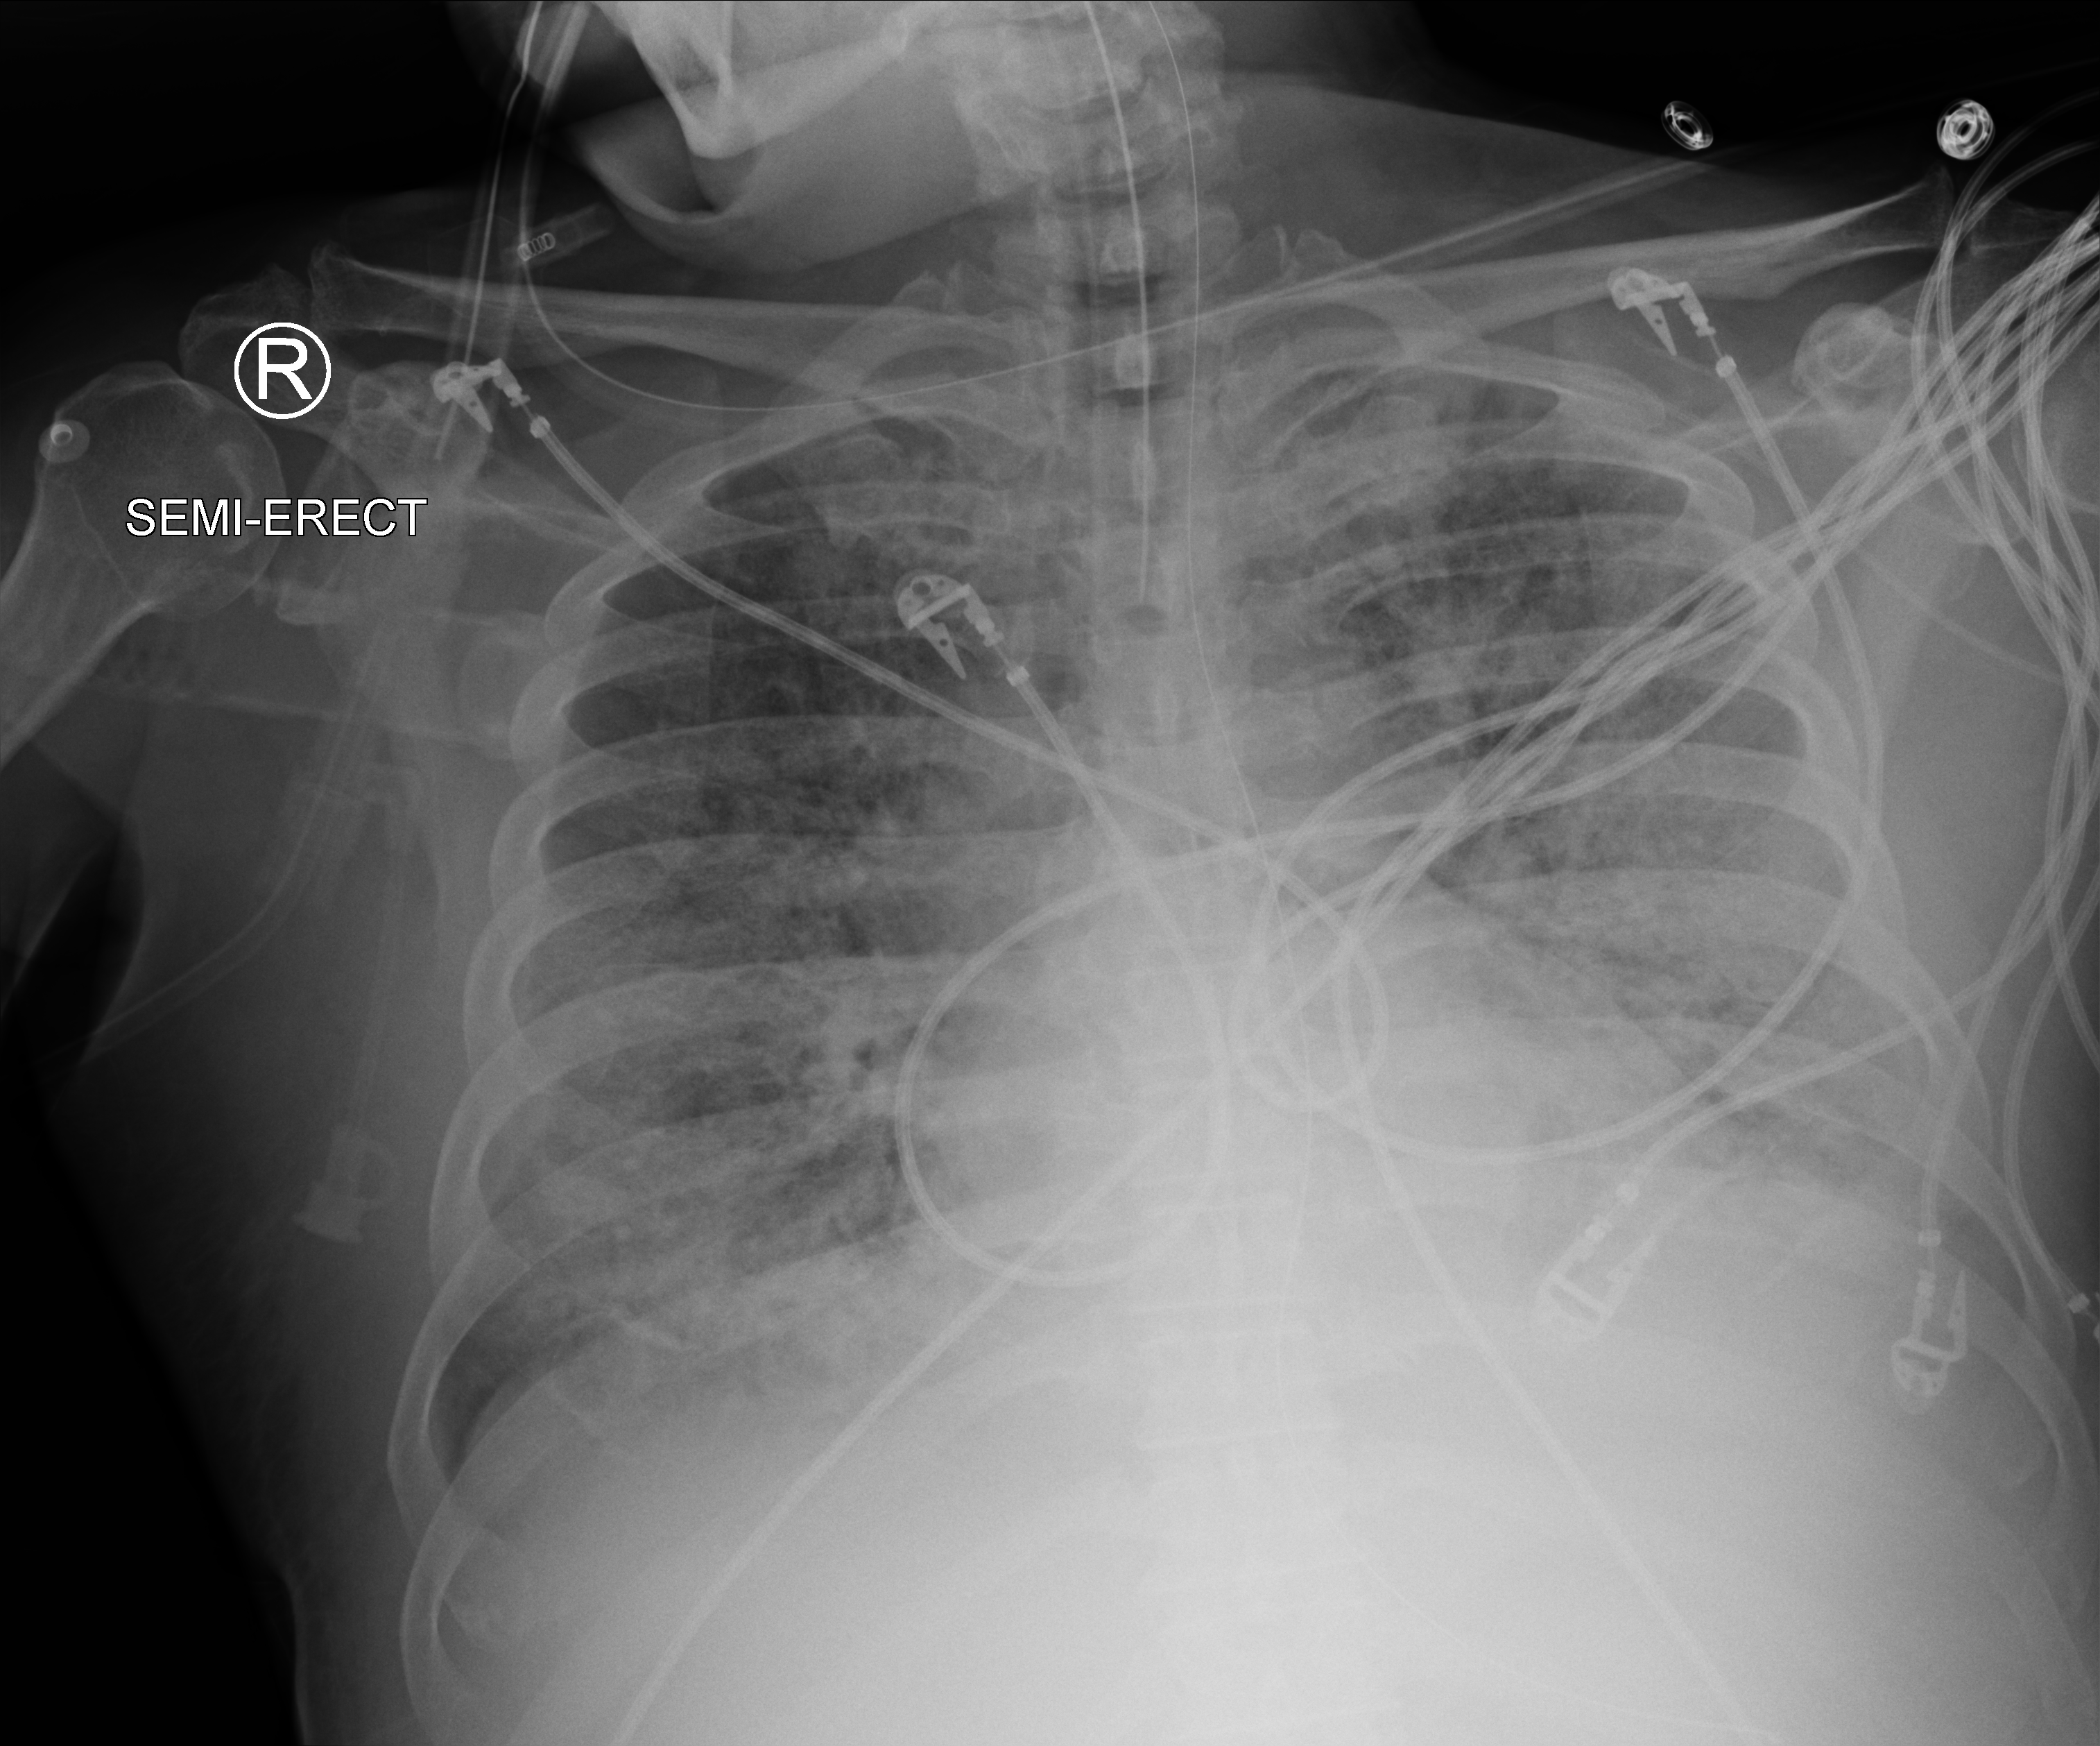
Bedside chest radiograph (computed radiography), anteroposterior (AP) projection. Male patient hospitalised with COVID-19, age 60–74 years.
From the hospital-stay record, not from the radiograph (when in the stay this image was taken is not recorded): mechanically ventilated during this hospital stay: yes.